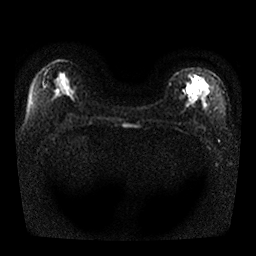
Breast MRI, one axial slice. Slice 15 of 25 in the series (ordered by position). Diffusion-weighted series; image 2 of 4 stored at this slice position (different b-values; order by instance number). 1.5 T. 4 mm slice thickness. 256 × 256 image matrix, field of view 330 × 330 mm. Female patient.
Structures marked on this image (outlined manually by an expert reader):
- tumour on diffusion-weighted imaging: bounding box <188,79,204,93> (left, top, right, bottom; pixels)